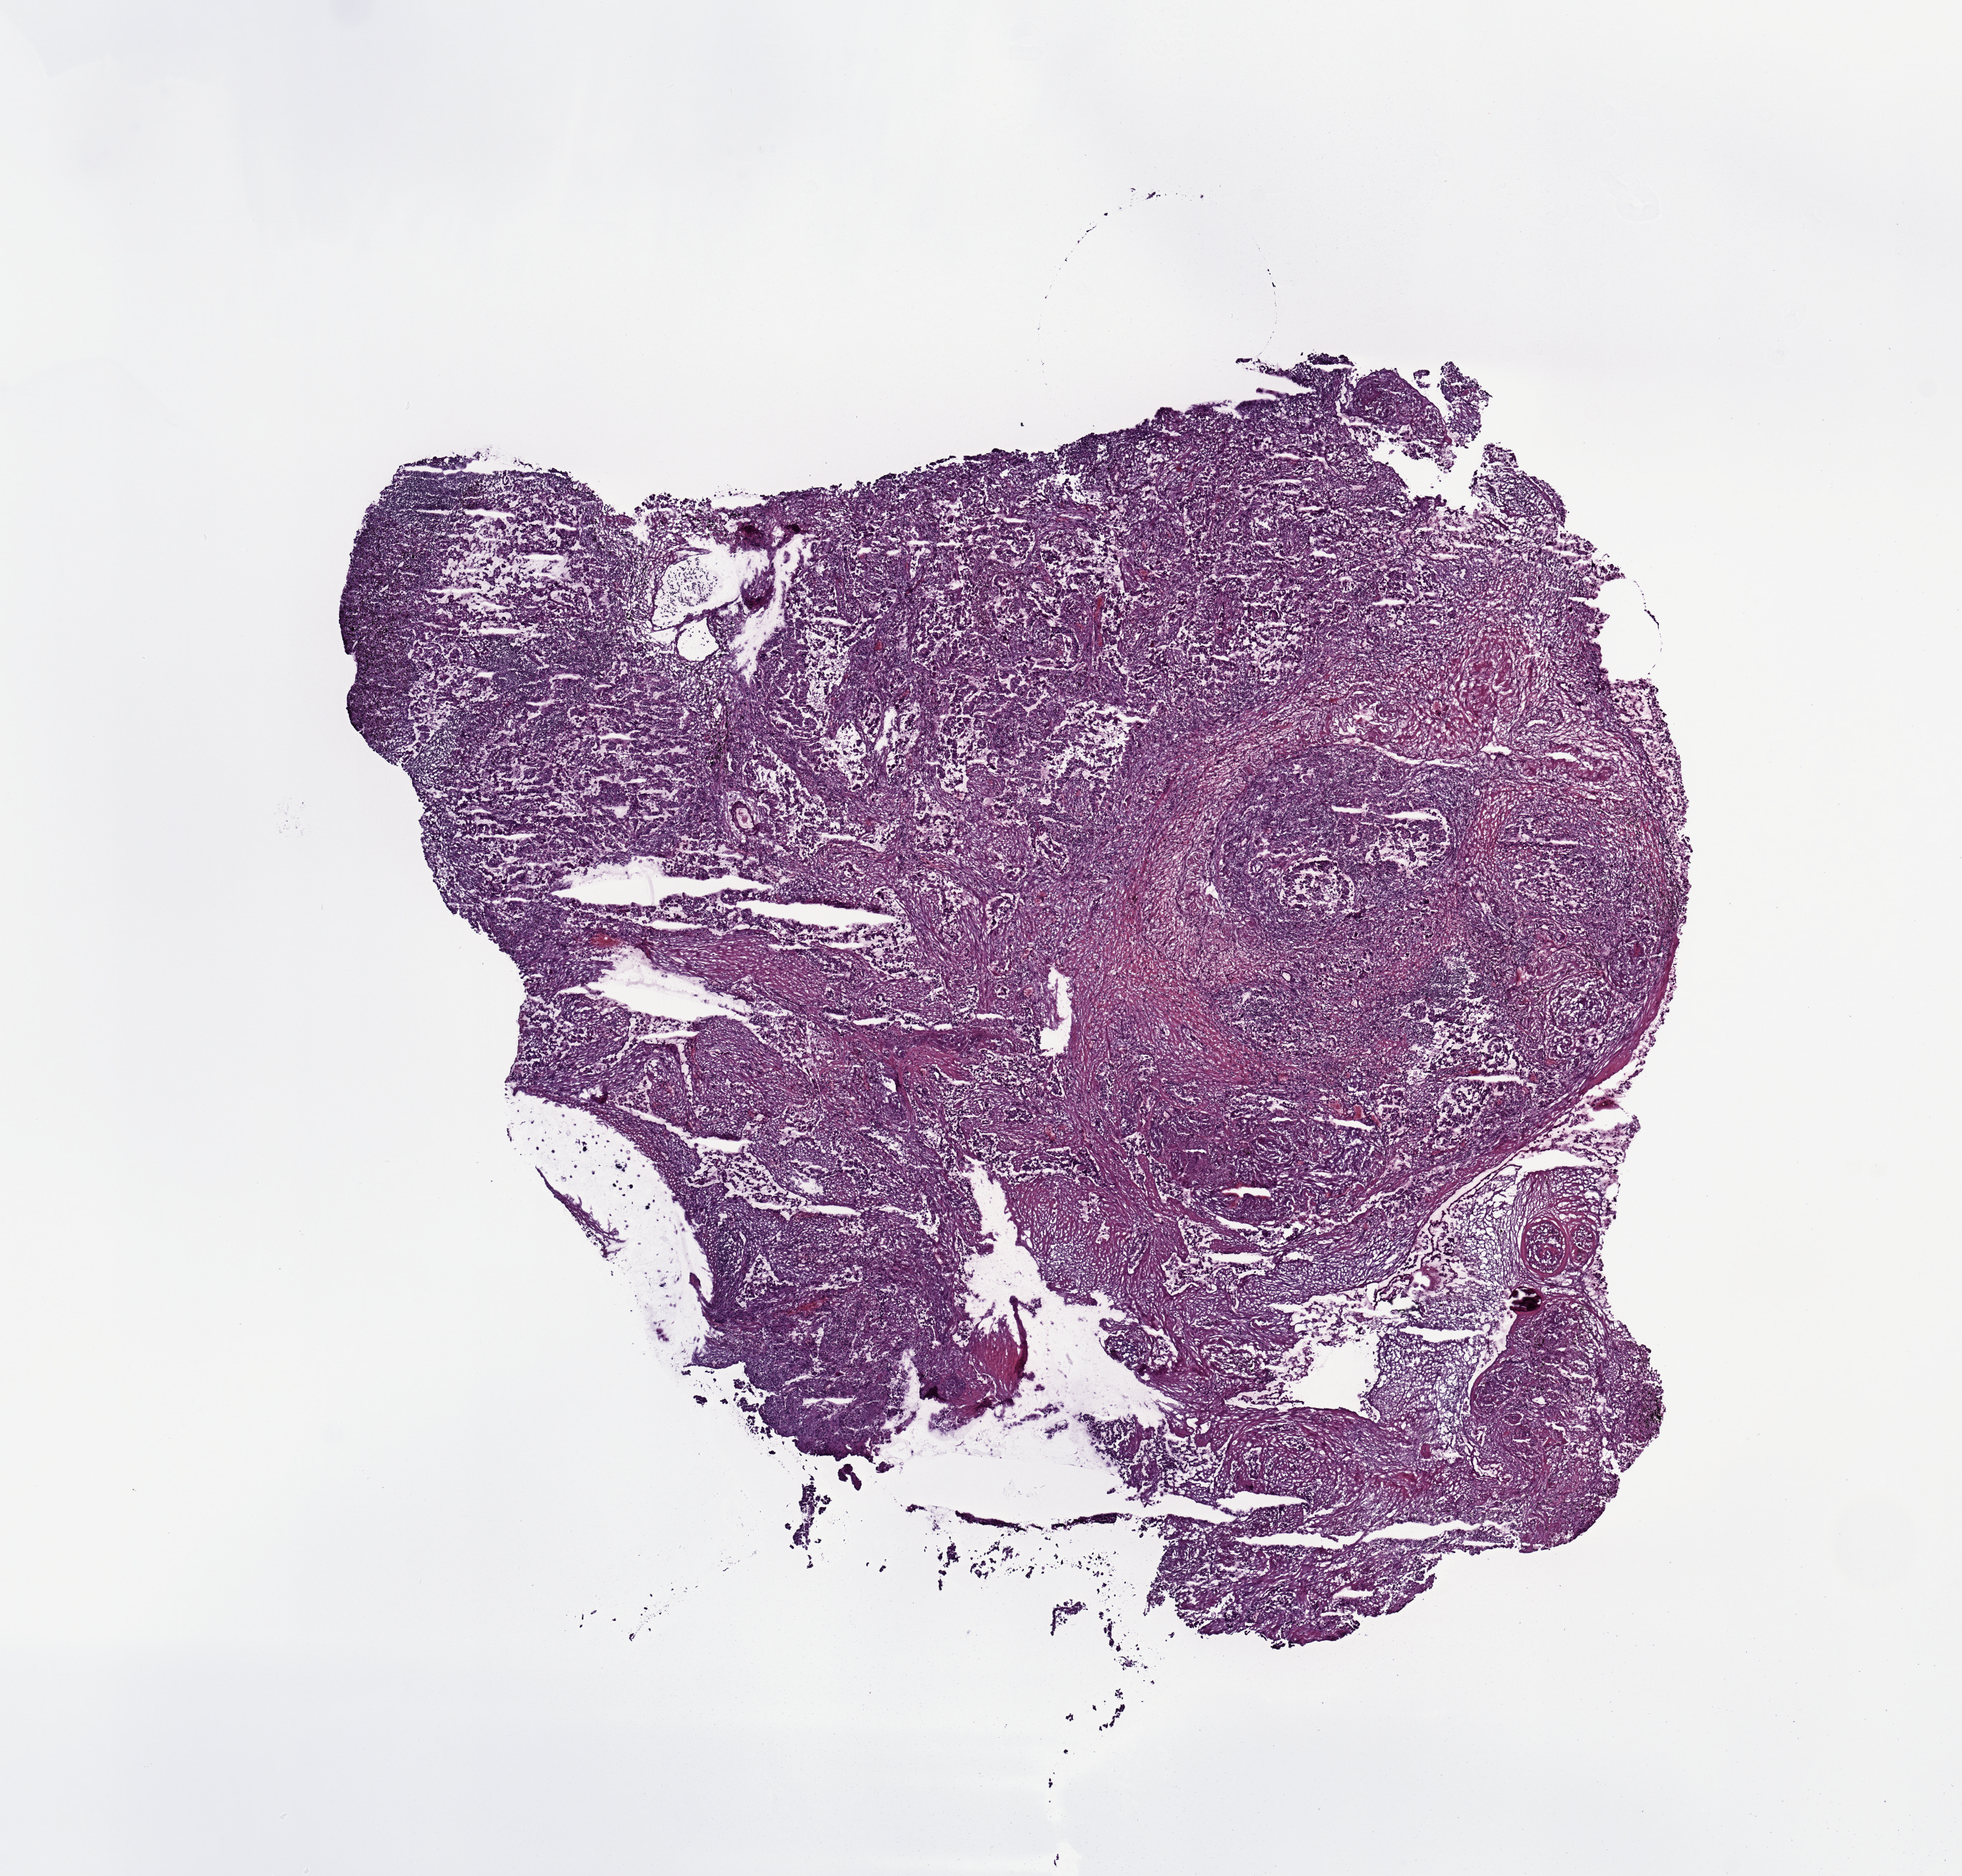
Whole-slide histology image, H&E, whole scanned area (about 10.8 x 10.4 mm, acquisition: 20x scan) shown as a low-resolution overview; tumour tissue sample, sampled site: lung. 72-year-old female patient. Histologic grade: G2 (moderately differentiated). Pathologist review of this section (percent, as recorded): tumour nuclei 80%, necrosis 10%.
Primary tumour site (as recorded): left upper lobe. AJCC pathologic stage: IB. Diagnosis: Adenocarcinoma, NOS.